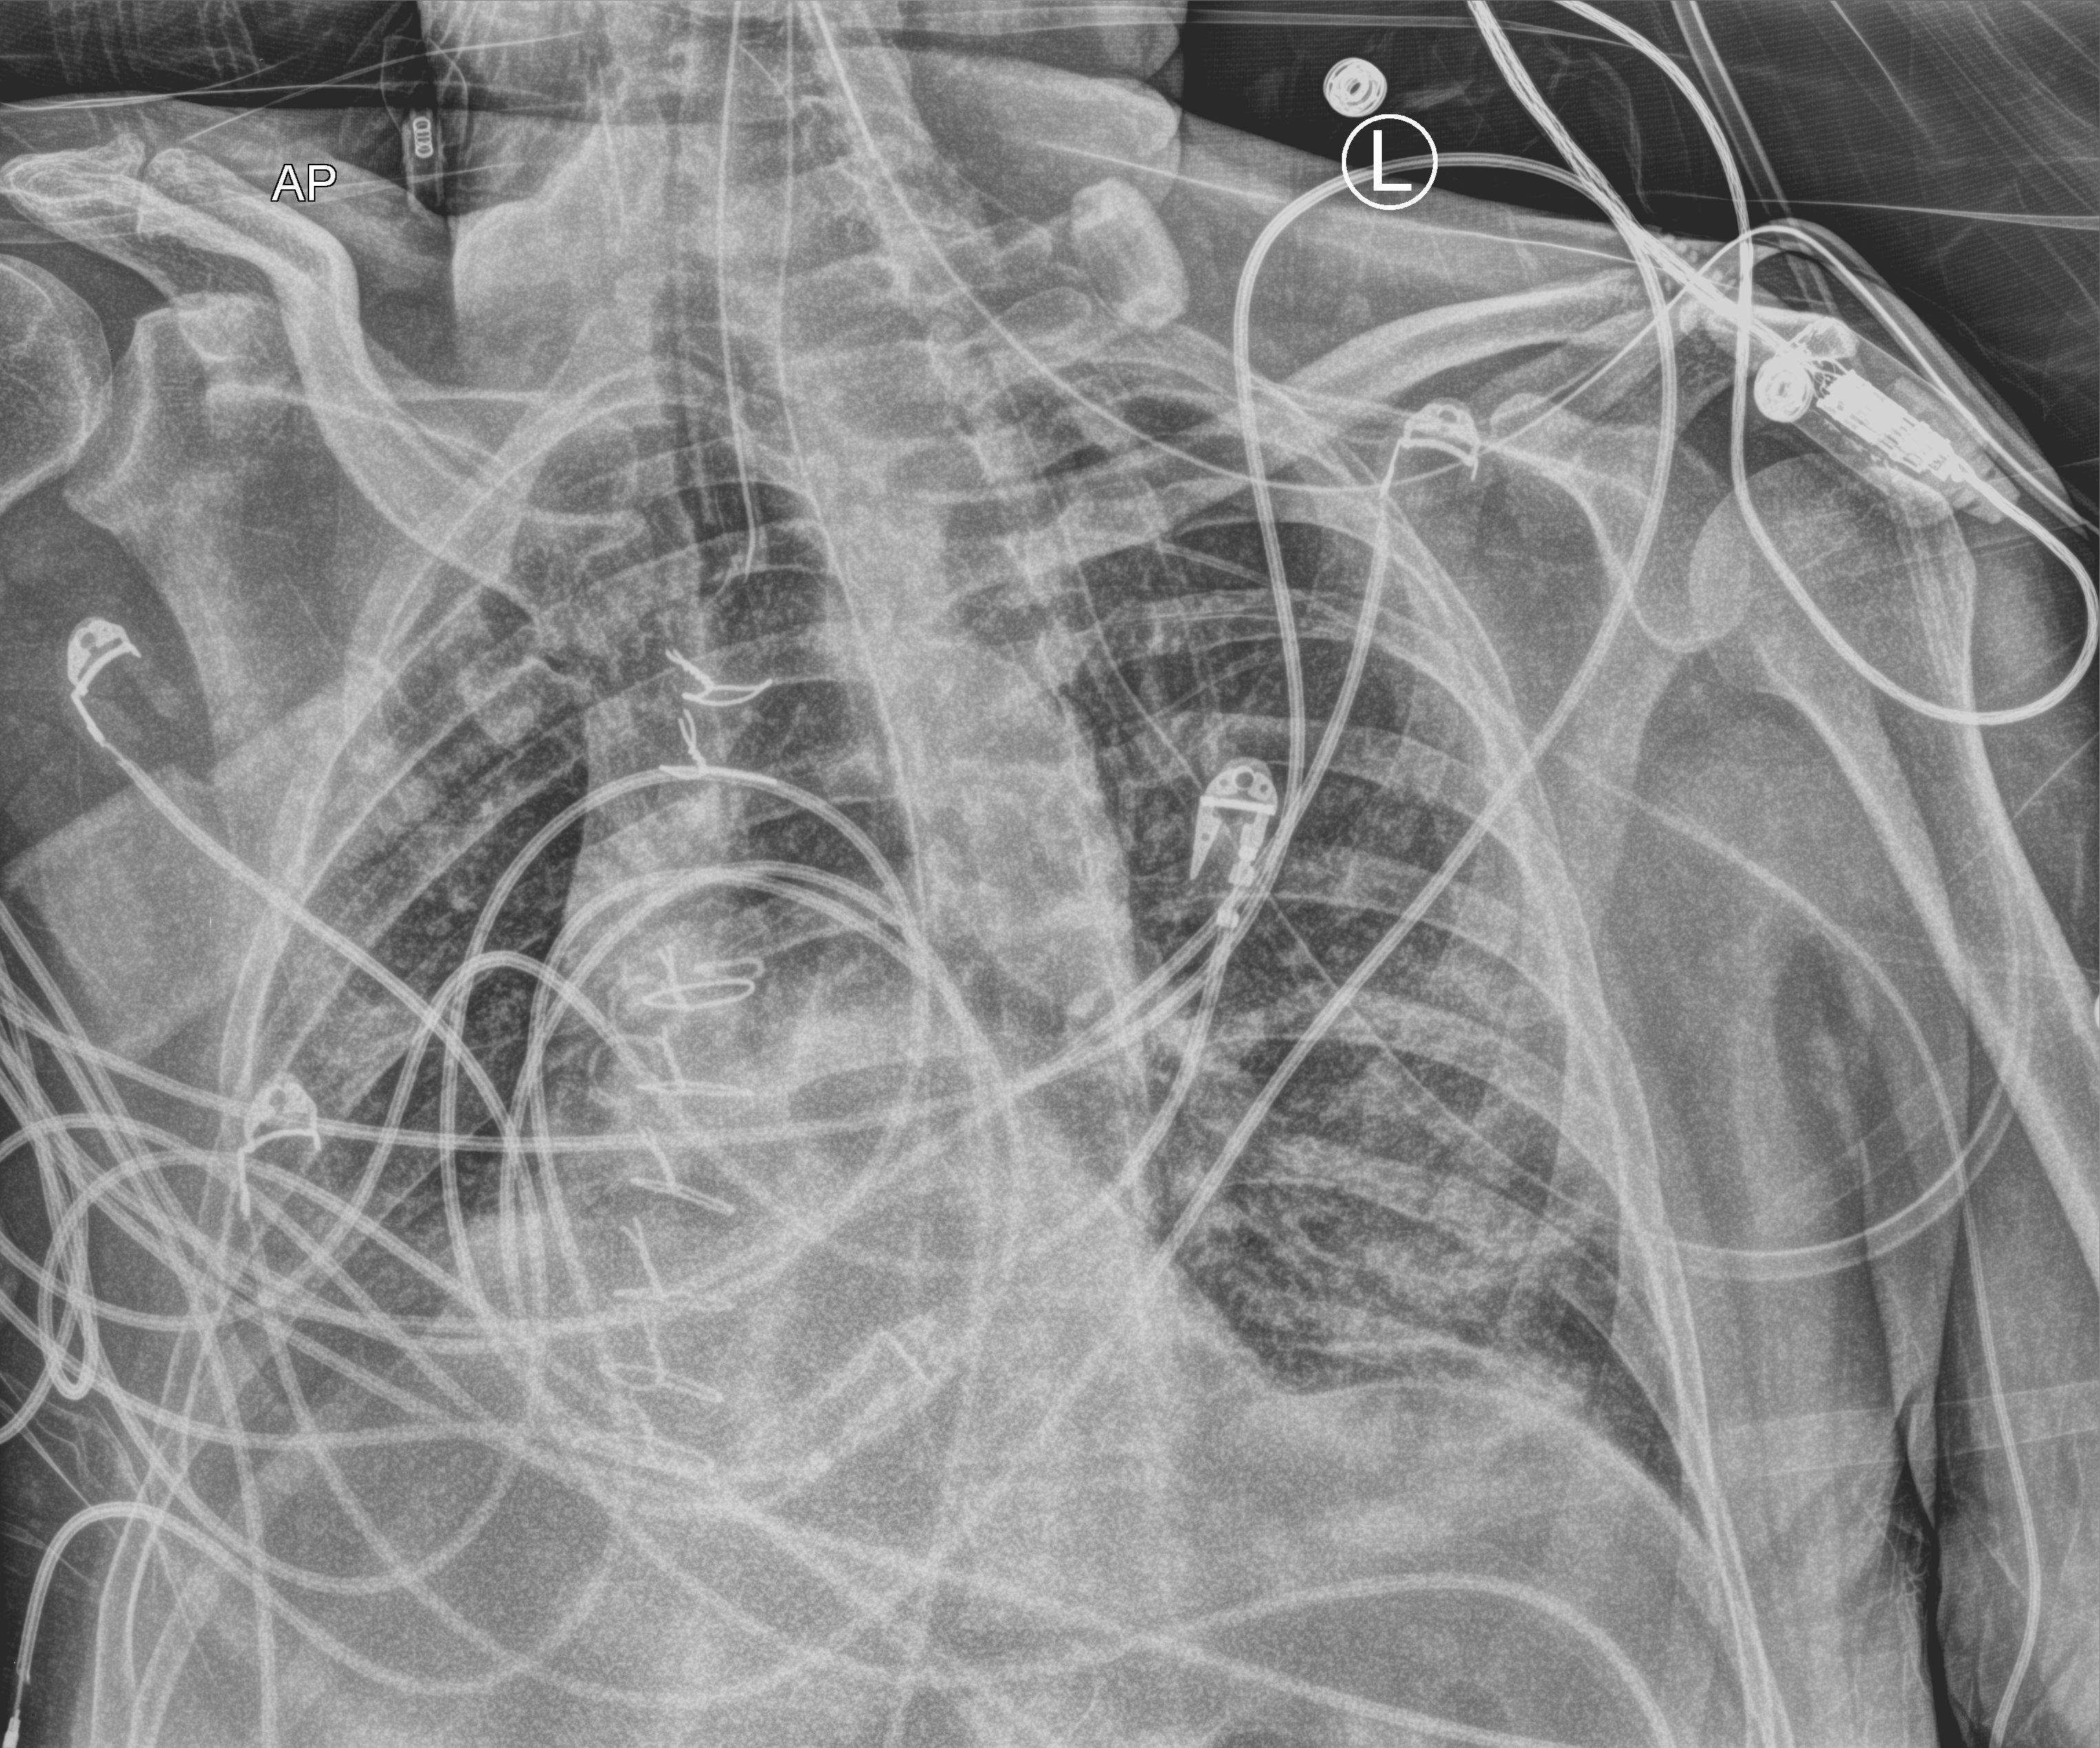
Bedside chest radiograph (computed radiography), anteroposterior (AP) projection. Patient hospitalised with COVID-19; male, aged 18–59 years.
Hospital-stay facts (about this admission, not read from this image; timing relative to this image not recorded): admitted to intensive care during this hospital stay: yes.